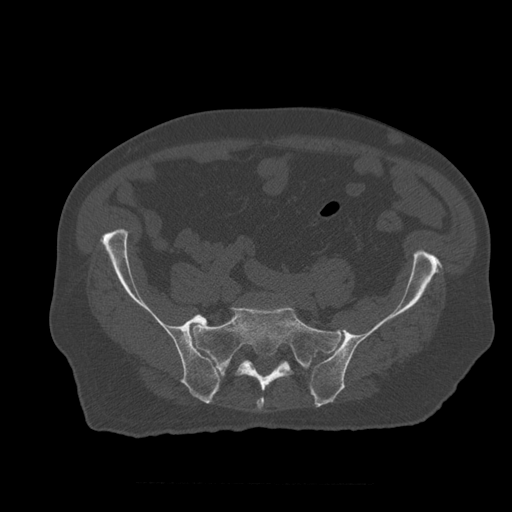
CT including the spine, one axial slice; bone window (W 1800 / L 400 HU); 1.25 mm slice thickness; 512 × 512 image matrix. Patient age 73 years. From the clinical record (not read from this slice): primary cancer: prostate; vertebrae with lytic lesions (as recorded): L2.
Structures marked on this image (semi-automatically segmented with operator editing):
- L5 vertebra: box from (x=213, y=365) to (x=220, y=376) px